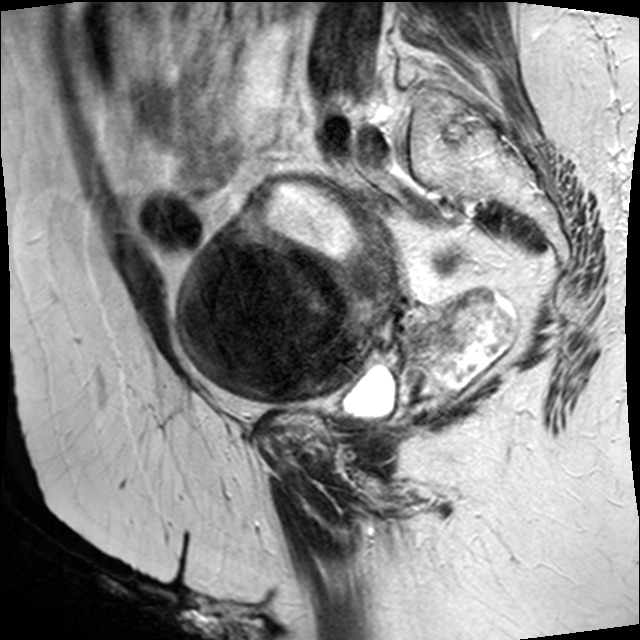
Pelvic MRI for cervical cancer, one sagittal slice; slice 17 of 45 in the series (ordered by position); T2-weighted; 1.5 T; TE 89 ms, TR 4610 ms; 4 mm slice thickness; 640 × 640 image matrix, field of view 260 × 260 mm. Female patient, age 50 years.
Outlined on this slice (expert manual segmentation):
- uterus and cervix: box from (x=169, y=175) to (x=522, y=420) px